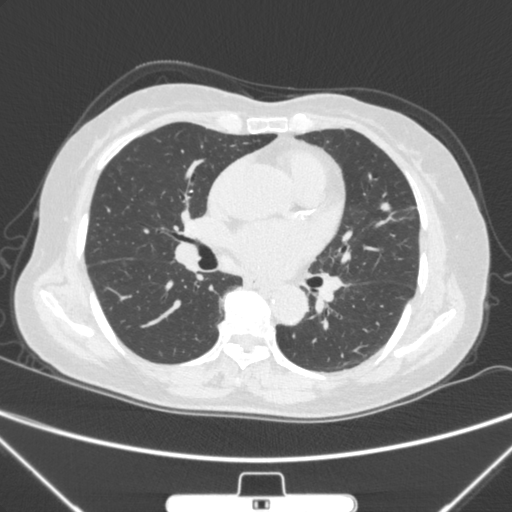
Chest CT, one axial slice; slice 145 of 300 in the series (ordered by position); lung window (W 1500 / L -600 HU); 1 mm slice thickness; 512 × 512 image matrix, field of view 350 × 350 mm. Female patient, age 70 years. Case-level facts recorded for this patient, not image findings: clinical TNM (as recorded): T1b N0 M0.
Structures marked on this image (bounding box drawn by a radiologist):
- lung tumour (recorded histology: adenocarcinoma): bounding box [x1, y1, x2, y2] px = [379, 196, 401, 220]